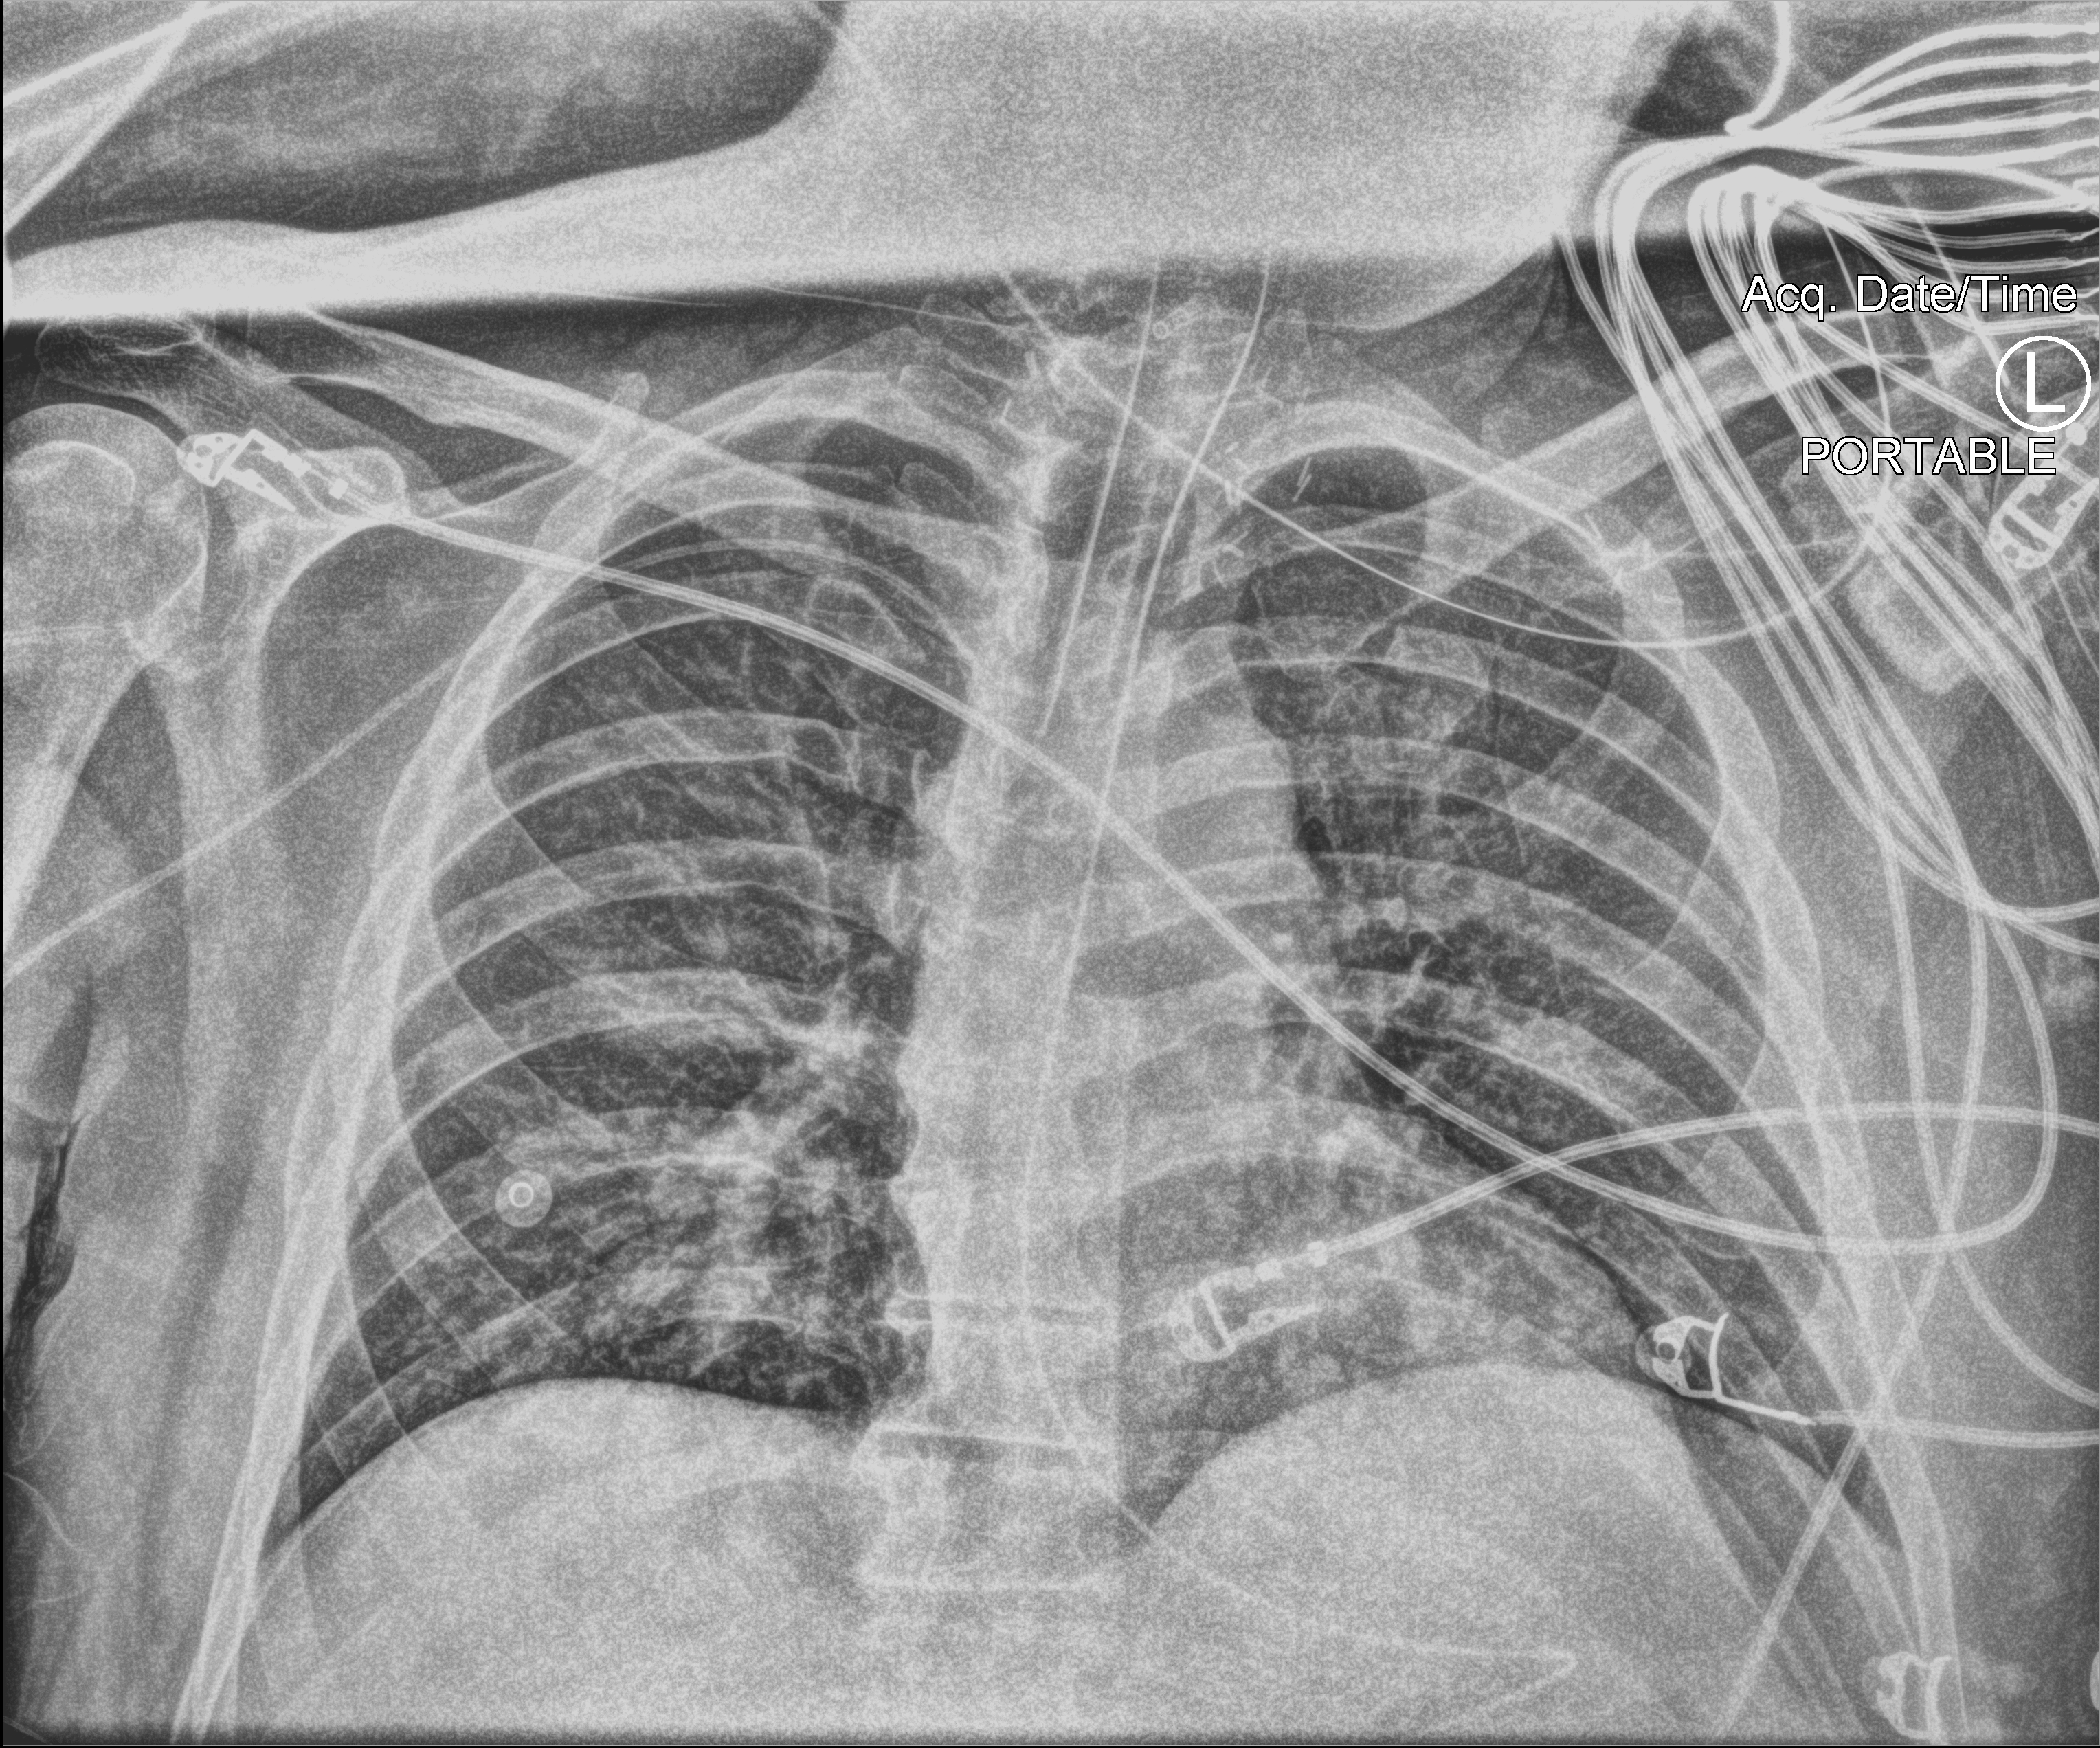
Bedside chest radiograph (computed radiography); anteroposterior (AP) projection. Patient hospitalised with COVID-19, aged 18–59 years.
Admission-level facts for this patient (not findings on this image; timing relative to this image not recorded):
- smoking status (admission record): never
- mechanically ventilated during this hospital stay: yes